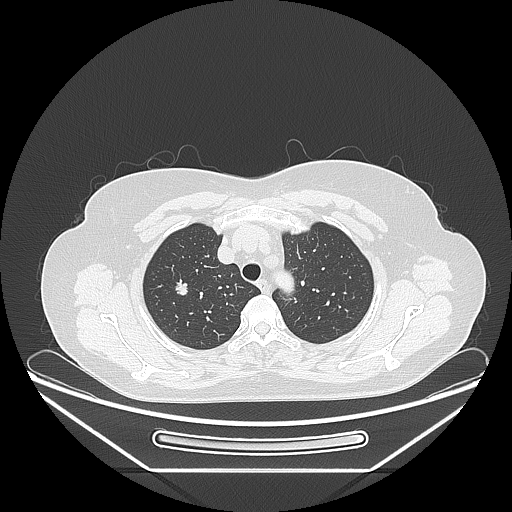
Chest CT, one axial slice; slice 198 of 236 in the series (ordered by position); 120 kVp; lung window (W 1500 / L -600 HU); 512 × 512 image matrix, field of view 433 × 433 mm. Patient: female, 60 years. From the clinical record (not read from this slice): clinical TNM (as recorded): T1c N0 M0; histopathological grade: G2-3.
Annotated regions visible in this slice (rectangle marked by the reading radiologist):
- lung tumour (recorded histology: adenocarcinoma): bounding box (x1, y1, x2, y2) in pixels: (172, 275, 192, 305)